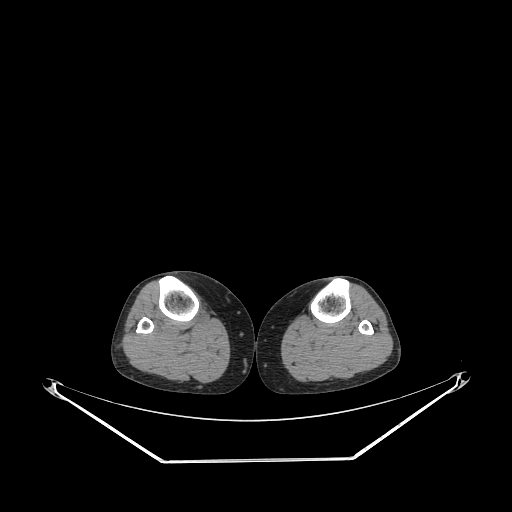
CT of an extremity soft-tissue mass (from a PET/CT study), one axial slice. Position 156 of 267 along the scan axis. Reconstruction kernel STANDARD. Soft-tissue window (W 400 / L 40 HU). 3.75 mm slice thickness. 512 × 512 image matrix. Female patient. Case-level facts recorded for this patient, not image findings: histological type: undifferentiated – high grade; grade: high; site of the primary tumour: right thigh.
Annotated regions visible in this slice (expert contour drawn on MRI and transferred to this co-registered scan by the dataset authors):
- gross tumour volume (mass): bounding box (x1, y1, x2, y2) in pixels: (196, 304, 211, 325)